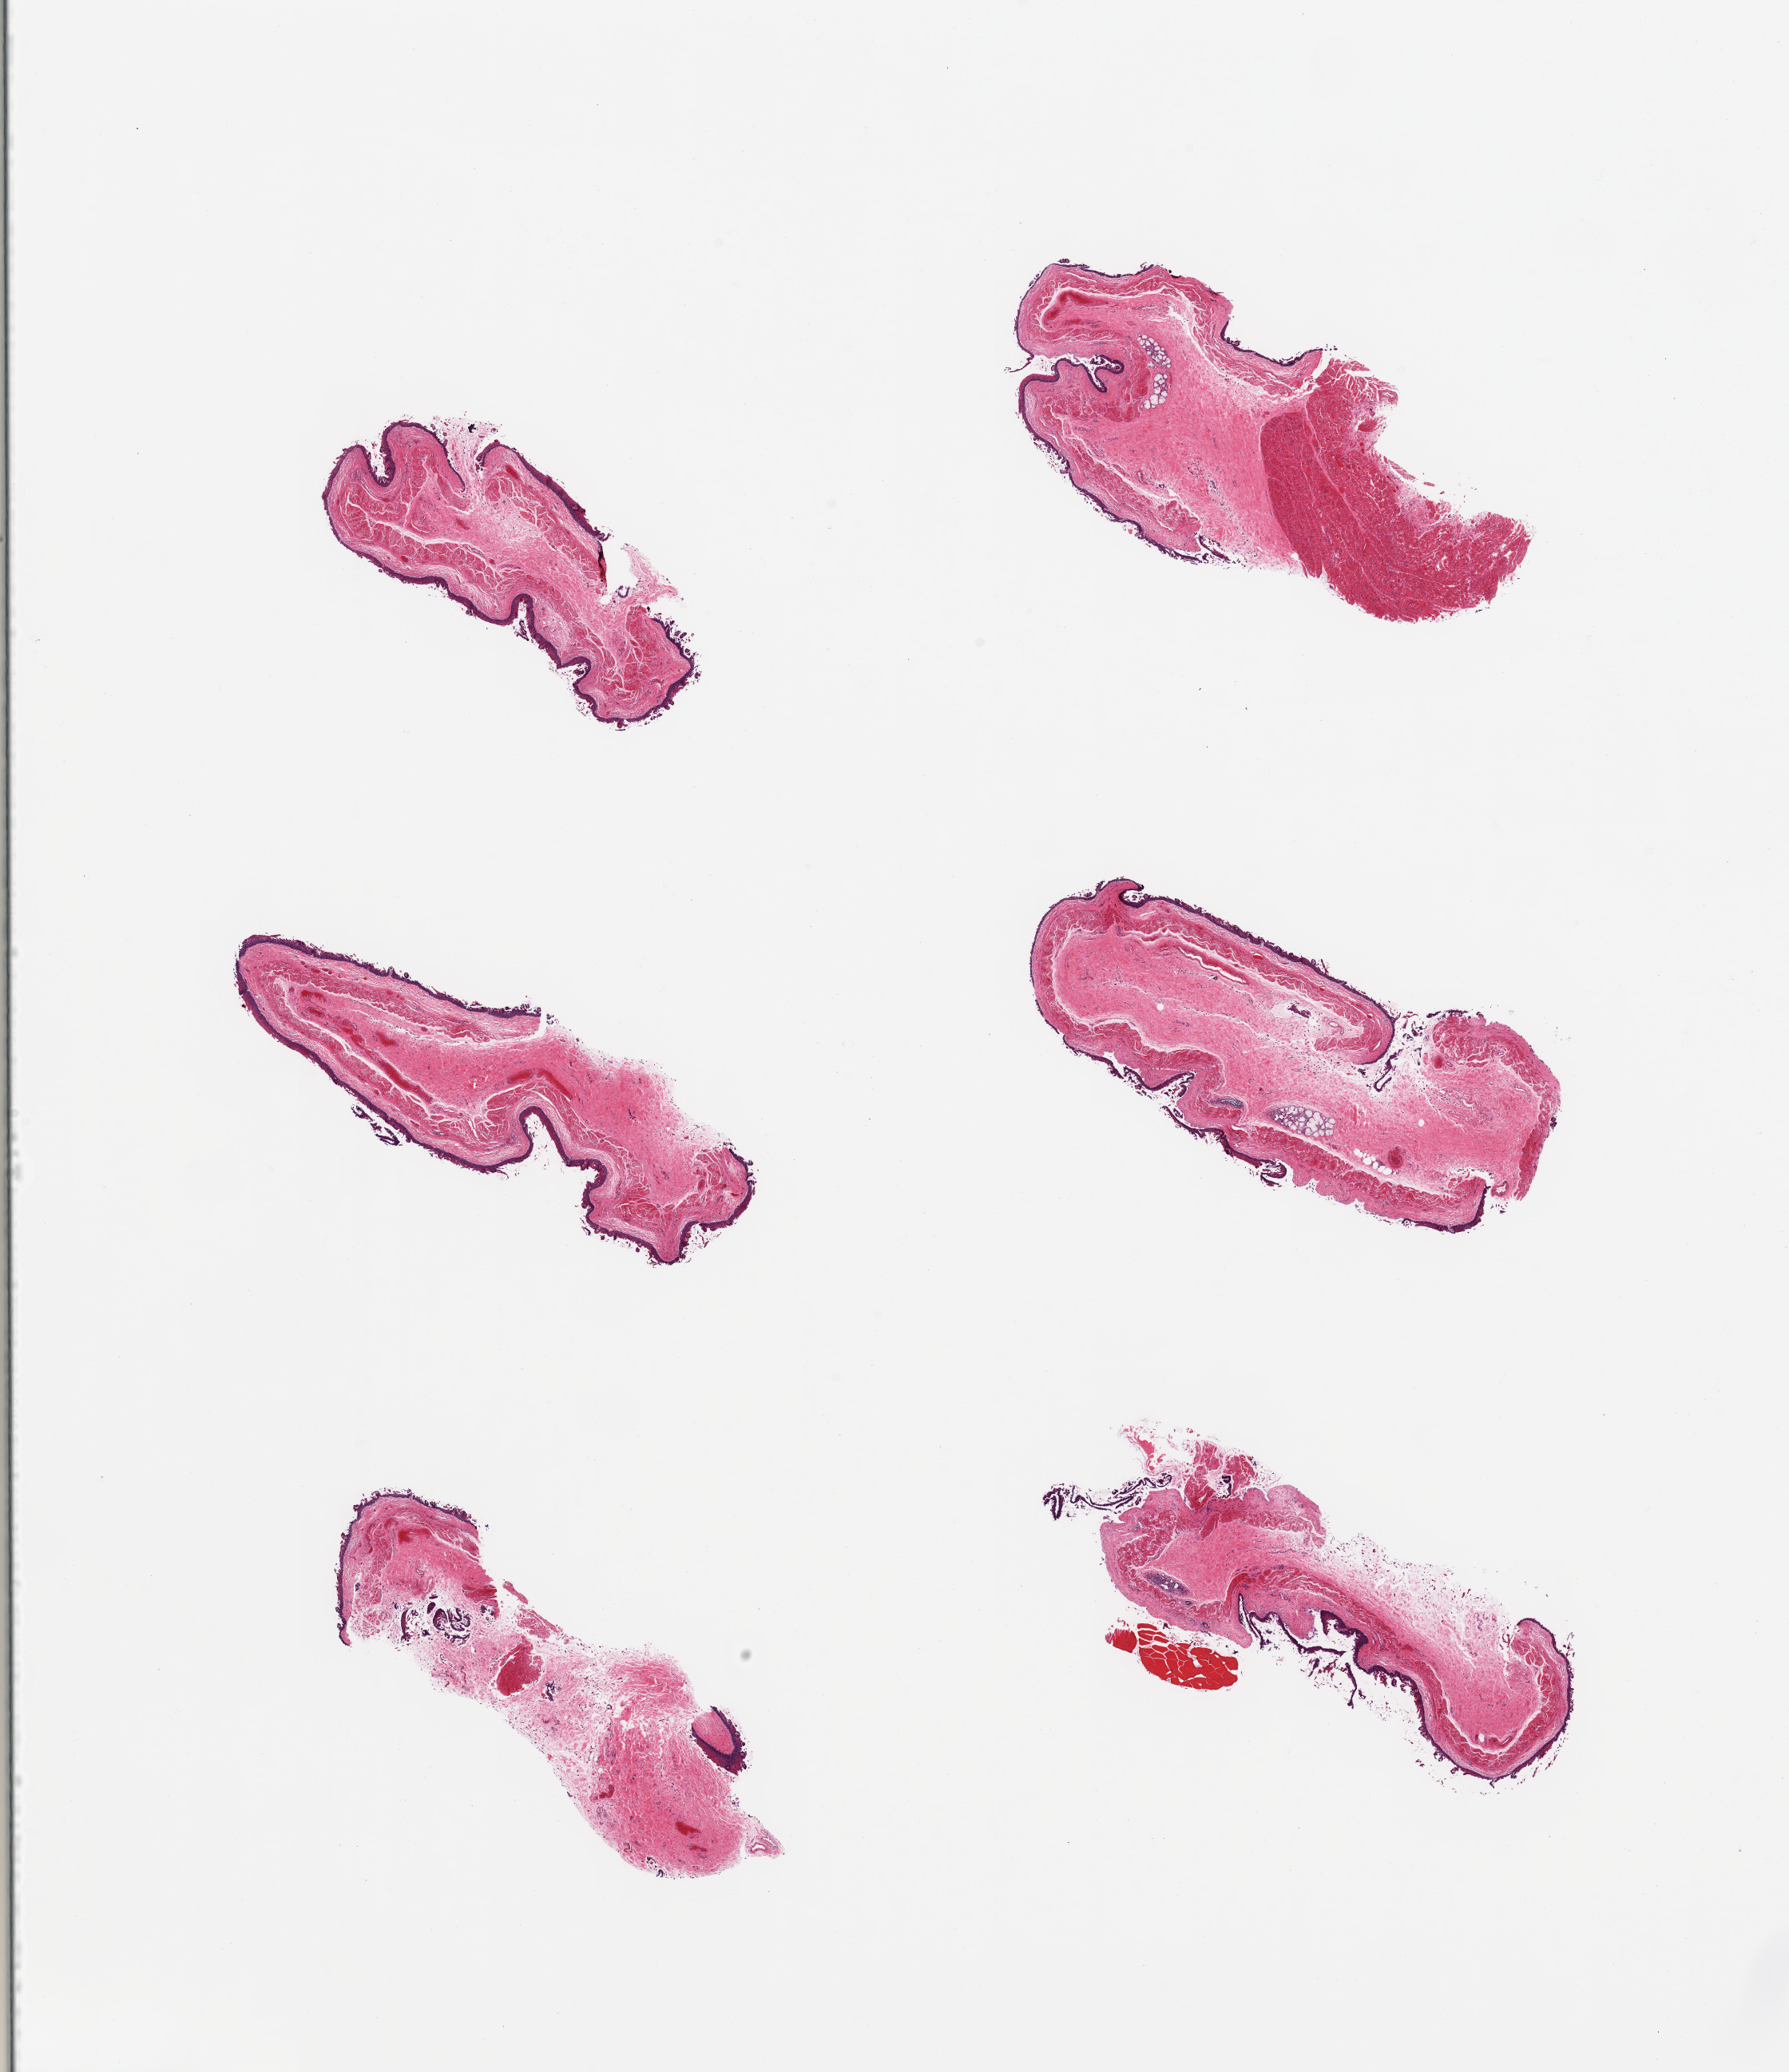
Hematoxylin and eosin (H&E) whole-slide image, brightfield, shown as a low-resolution overview of the whole scanned area (about 17.7 x 20.5 mm, acquisition: 20x scan); PAXgene-fixed paraffin-embedded (PFPE) section; sampled site (target tissue): esophageal mucous membrane; donor tissue sample. Donor: female.
- pathologist's review note for this sample: 6 pieces, target squamous mucosa partially sloughing, ~70 microns, <10% thickness